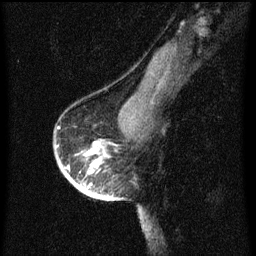
Breast MRI (dynamic contrast-enhanced), one sagittal slice. Slice 45 of 60 in the series (ordered by position). Dynamic contrast-enhanced series, image 2 of 3 at this slice position (ordered by acquisition). 1.5 T. TE 4.2 ms, TR 8 ms. 256 × 256 image matrix, field of view 180 × 180 mm. Female patient, age 56 years.
Annotated regions visible in this slice (semi-automatically segmented with operator editing):
- analysis volume of interest (the breast-tissue region the enhancement analysis was run in; not a lesion): box from (x=54, y=128) to (x=119, y=199) px
- tumour enhancement mask (voxels above the 70 % enhancement threshold inside the analysis volume of interest): (x=56, y=128)–(x=116, y=199)